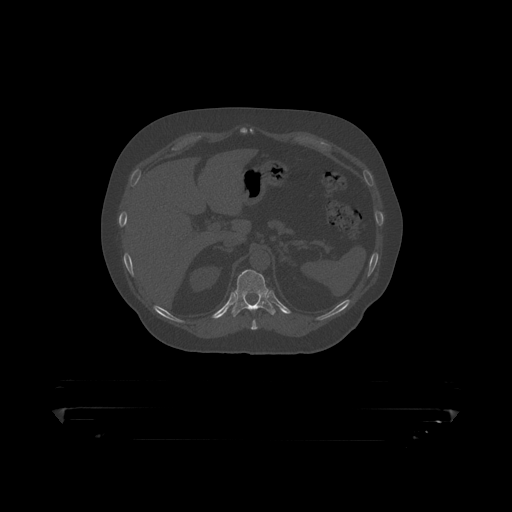
CT including the spine, one axial slice; position 198 of 390 along the scan axis; reconstruction kernel STANDARD; bone window (W 1800 / L 400 HU); 512 × 512 image matrix. Male patient, age 60 years. Case-level facts recorded for this patient, not image findings: primary cancer: prostate.
Structures marked on this image (semi-automatically segmented with operator editing):
- T11 vertebra: bounding box <228,270,289,316> (left, top, right, bottom; pixels)